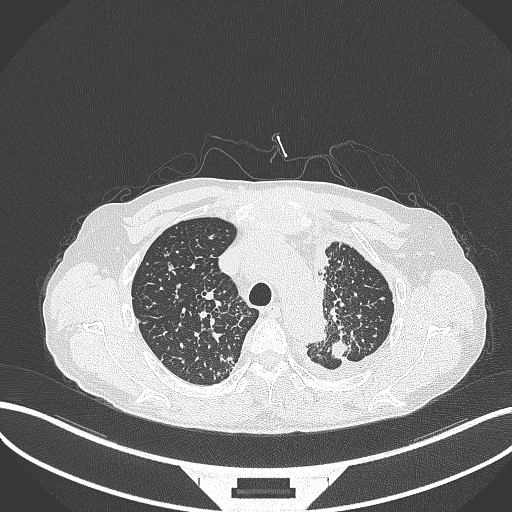
Chest CT, one axial slice; position 273 of 325 along the scan axis; lung window (W 1500 / L -600 HU); 1 mm slice thickness; 512 × 512 image matrix, field of view 400 × 400 mm. Patient: male, 58 years. Case-level facts recorded for this patient, not image findings: clinical TNM (as recorded): T1c N3 M1.
Annotated regions visible in this slice (rectangle marked by the reading radiologist):
- lung tumour (recorded histology: adenocarcinoma): bounding box [x1, y1, x2, y2] px = [325, 336, 355, 361]